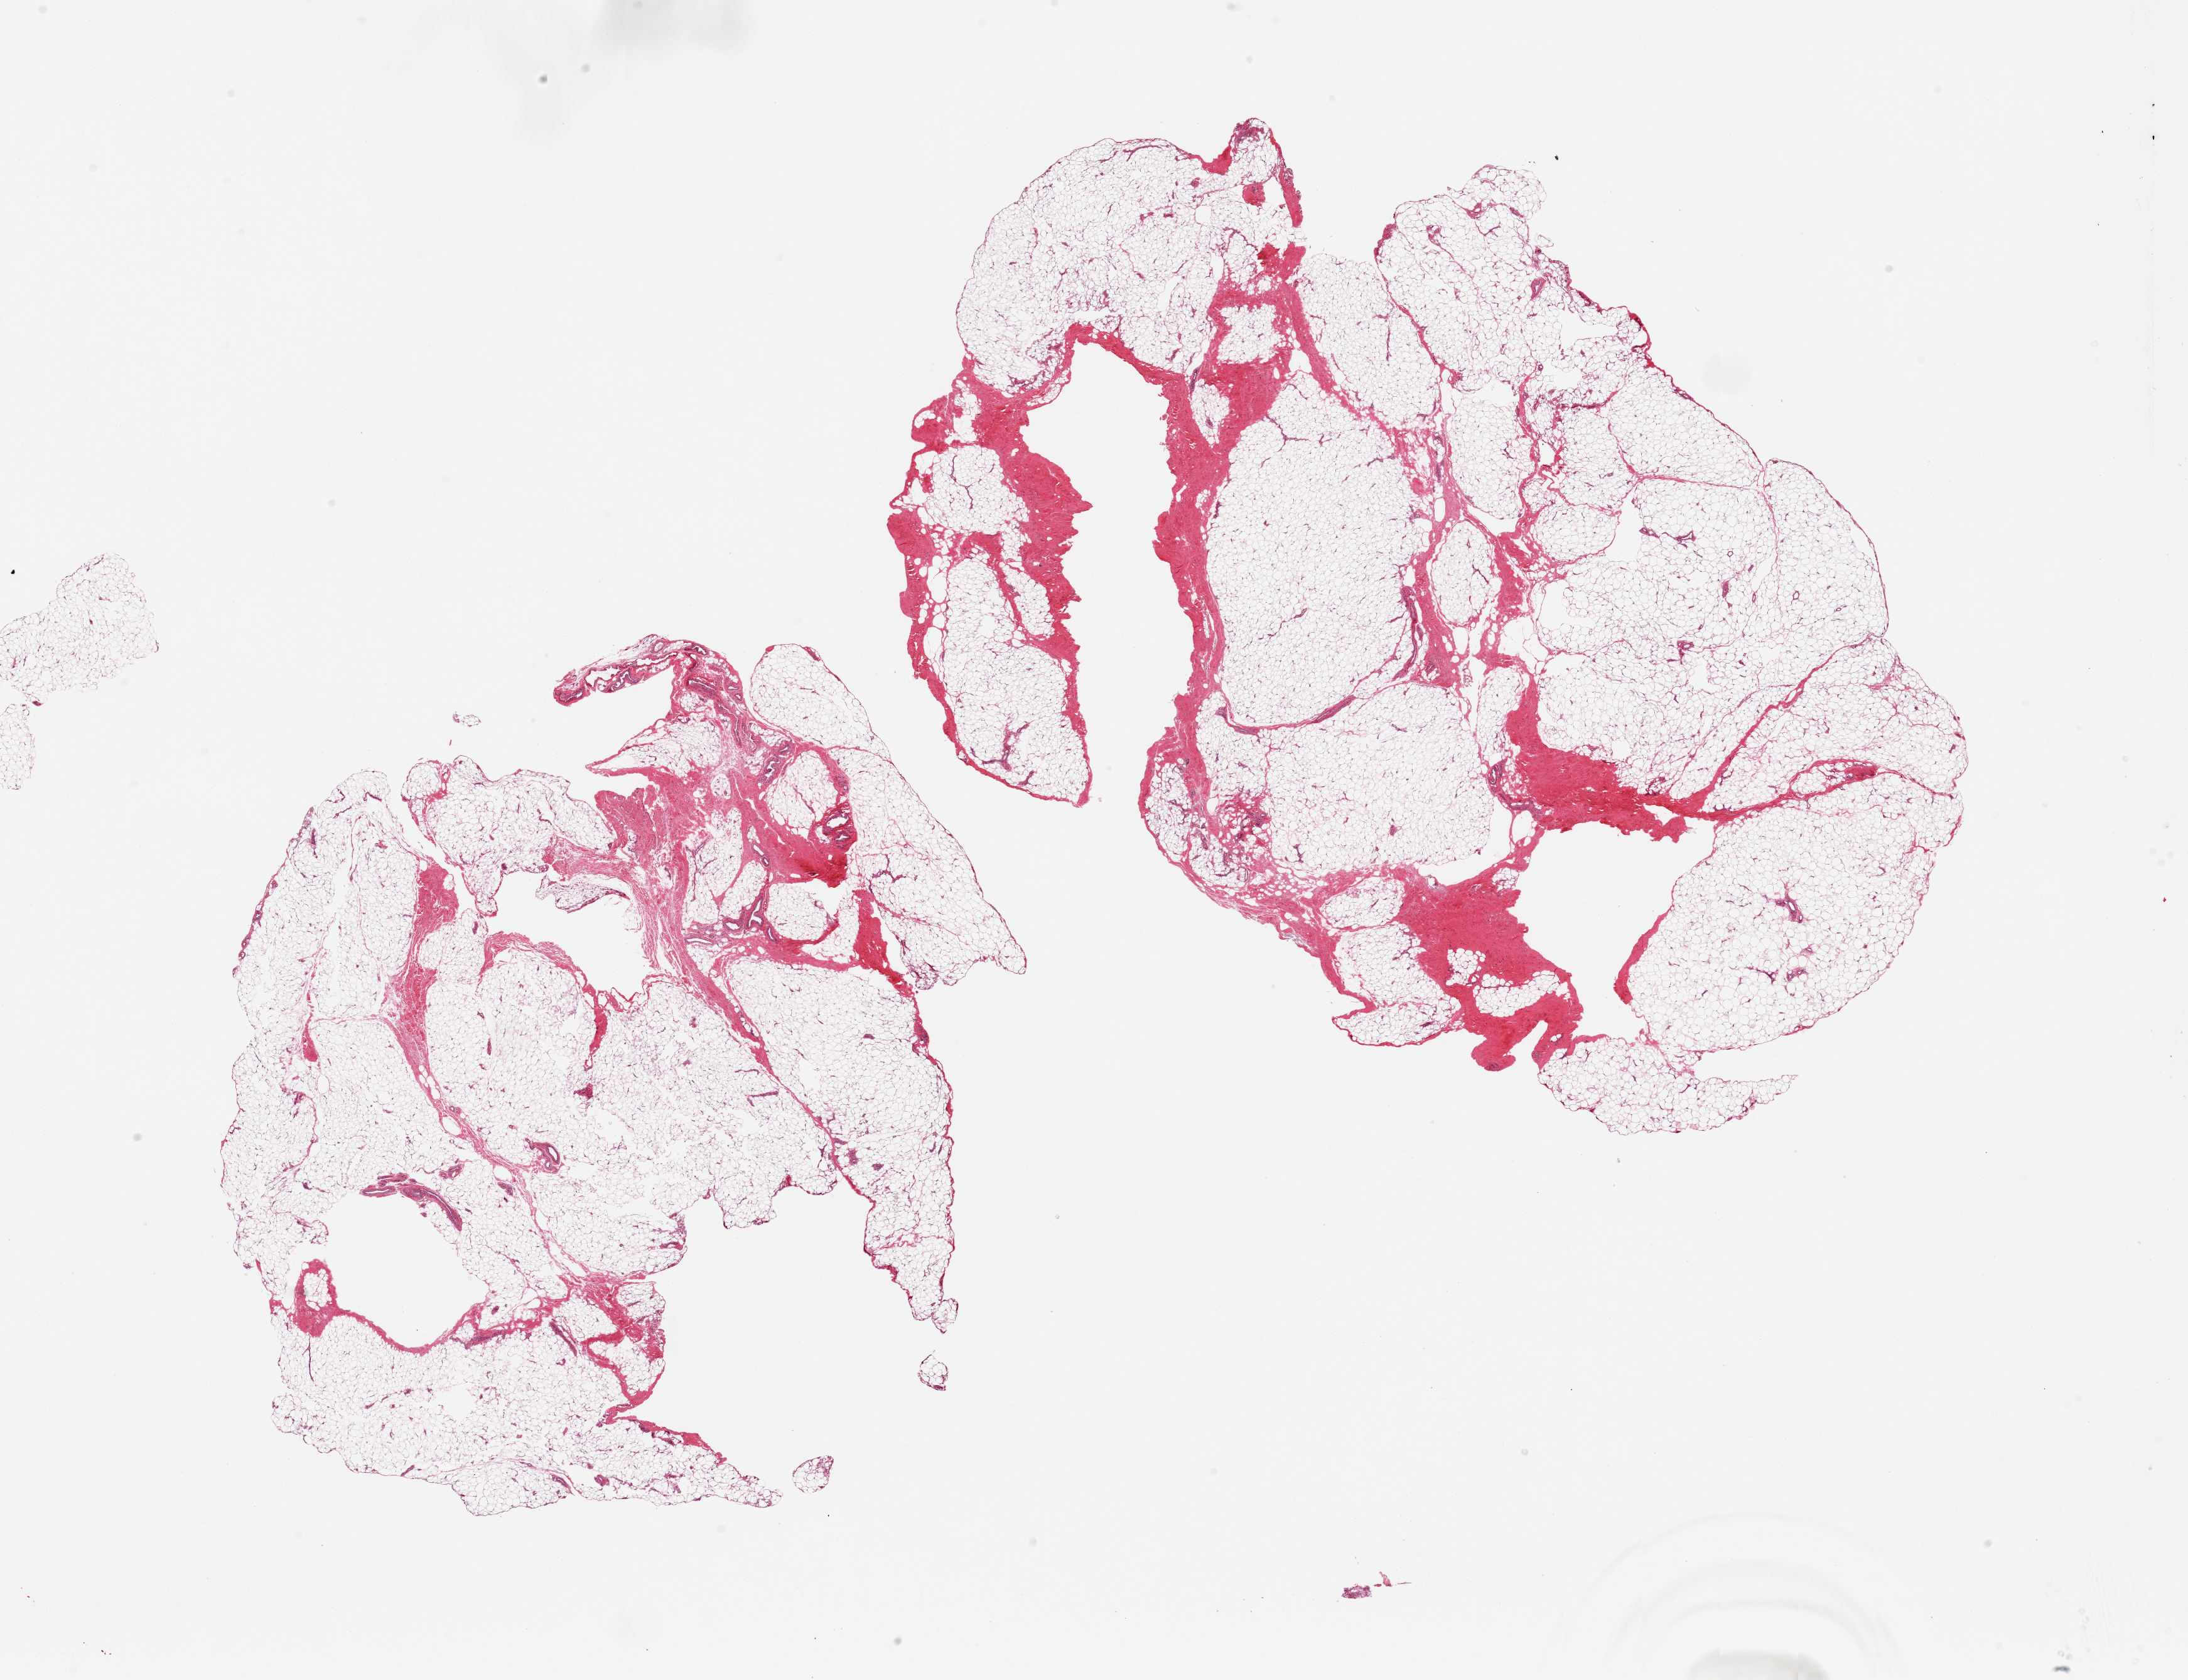
Hematoxylin and eosin (H&E) whole-slide image, whole scanned area (about 27.6 x 21.2 mm) shown as a low-resolution overview. PAXgene-fixed paraffin-embedded (PFPE) section. Target tissue: adipose tissue. Tissue donor sample. Male donor.
Reviewer comment on this tissue sample: 2 pieces, ~15-20% fascia/vascular elements.